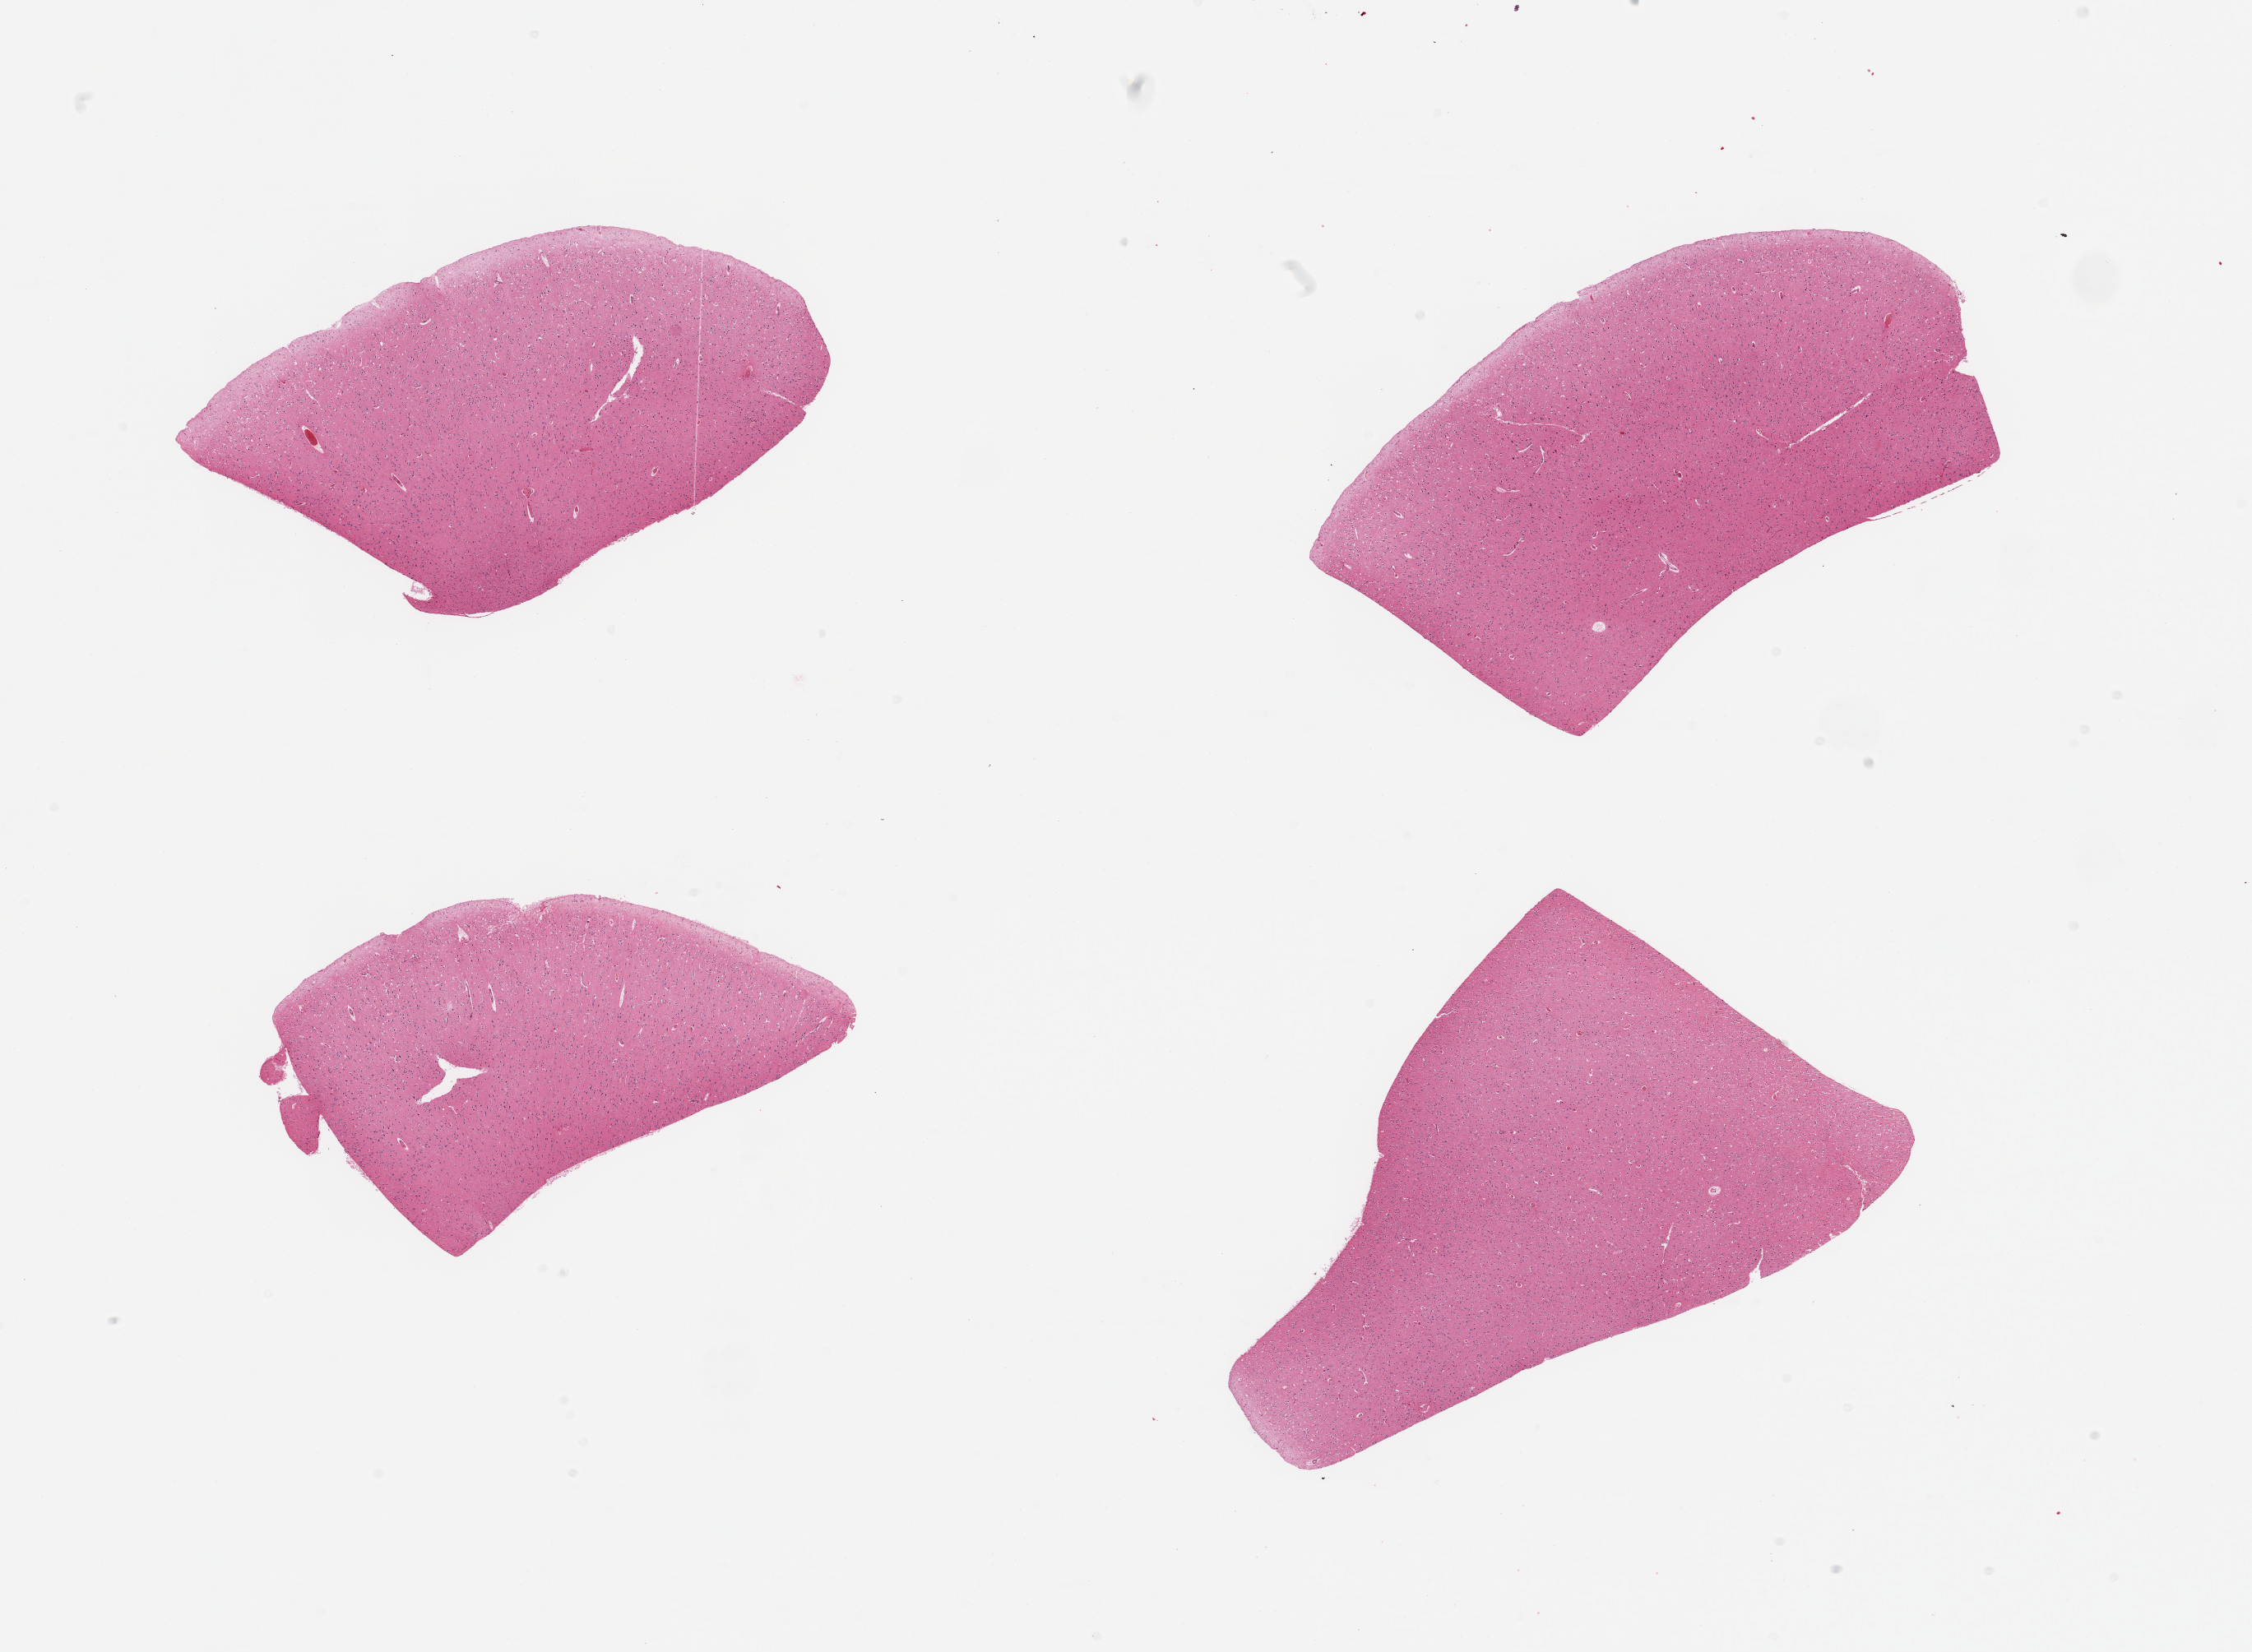
H&E whole-slide image — low-resolution overview of the scanned area, about 21.7 x 15.9 mm; PAXgene-fixed paraffin-embedded (PFPE) section; sampled site (target tissue): cerebral cortex; tissue donor sample. Donor sex: male.
Review note (as recorded): 4 pieces.